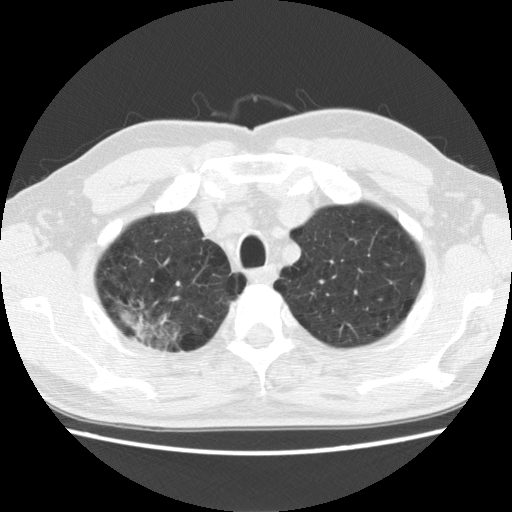
Axial slice from a low-dose chest CT screening exam. First (baseline) screen. Lung window (W 1500 / L -600 HU). 2.5 mm slice thickness. Slice 25 of 142 in the series. 512 × 512 image matrix, field of view 340 × 340 mm. Male, age 64 years at enrolment. Former smoker at enrolment.
Lesion marked by an expert reader, bounding box [x1, y1, x2, y2] px = [108, 289, 196, 362]. Reader record for this screening exam (exam-level; its link to the box is not recorded): non-calcified nodule or mass ≥4 mm, right upper lobe, 39 × 31 mm, spiculated (stellate) margins, mixed attenuation. Official screen result: positive, change unspecified: nodule(s) >= 4 mm or enlarging nodule(s), mass(es), or other non-specific abnormalities suspicious for lung cancer. Participant outcome: lung cancer diagnosed 74 days after this screen — adenocarcinoma, NOS, right upper lobe, moderately differentiated (G2), stage IB (AJCC 6th edition), 40 mm at pathology.